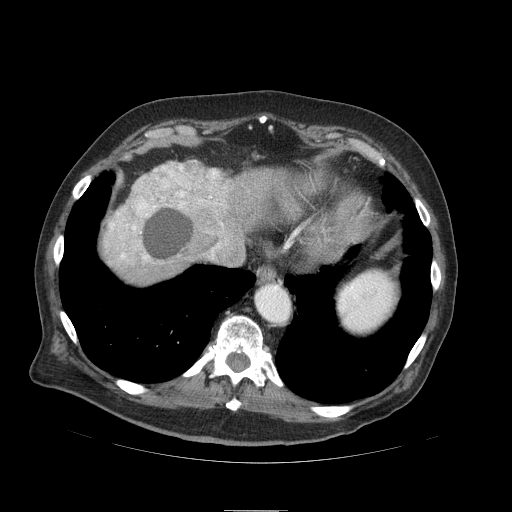
Contrast-enhanced abdominal CT (liver protocol), one axial slice. Position 79 of 103 along the scan axis. Reconstruction kernel STANDARD. 120 kVp. Soft-tissue window (W 400 / L 40 HU). 2.5 mm slice thickness. 512 × 512 image matrix, field of view 440 × 440 mm. Case-level facts recorded for this patient, not image findings: diagnosis: hepatocellular carcinoma (patient treated with transarterial chemoembolisation; whether this scan precedes or follows treatment is not stated here); TNM stage (as recorded): Stage-IIIA; Child-Pugh class: B; tumour nodularity: multinodular; tumour size: 13 cm.
Annotated regions visible in this slice (semi-automatic segmentation, software-assisted and operator-edited):
- liver parenchyma outside the tumour (the mass and vessels are separate outlines, so this box may not span the whole liver): bounding box [x1, y1, x2, y2] px = [100, 160, 294, 284]
- mass: [105, 162, 229, 264]
- liver vessels: [123, 171, 217, 258]